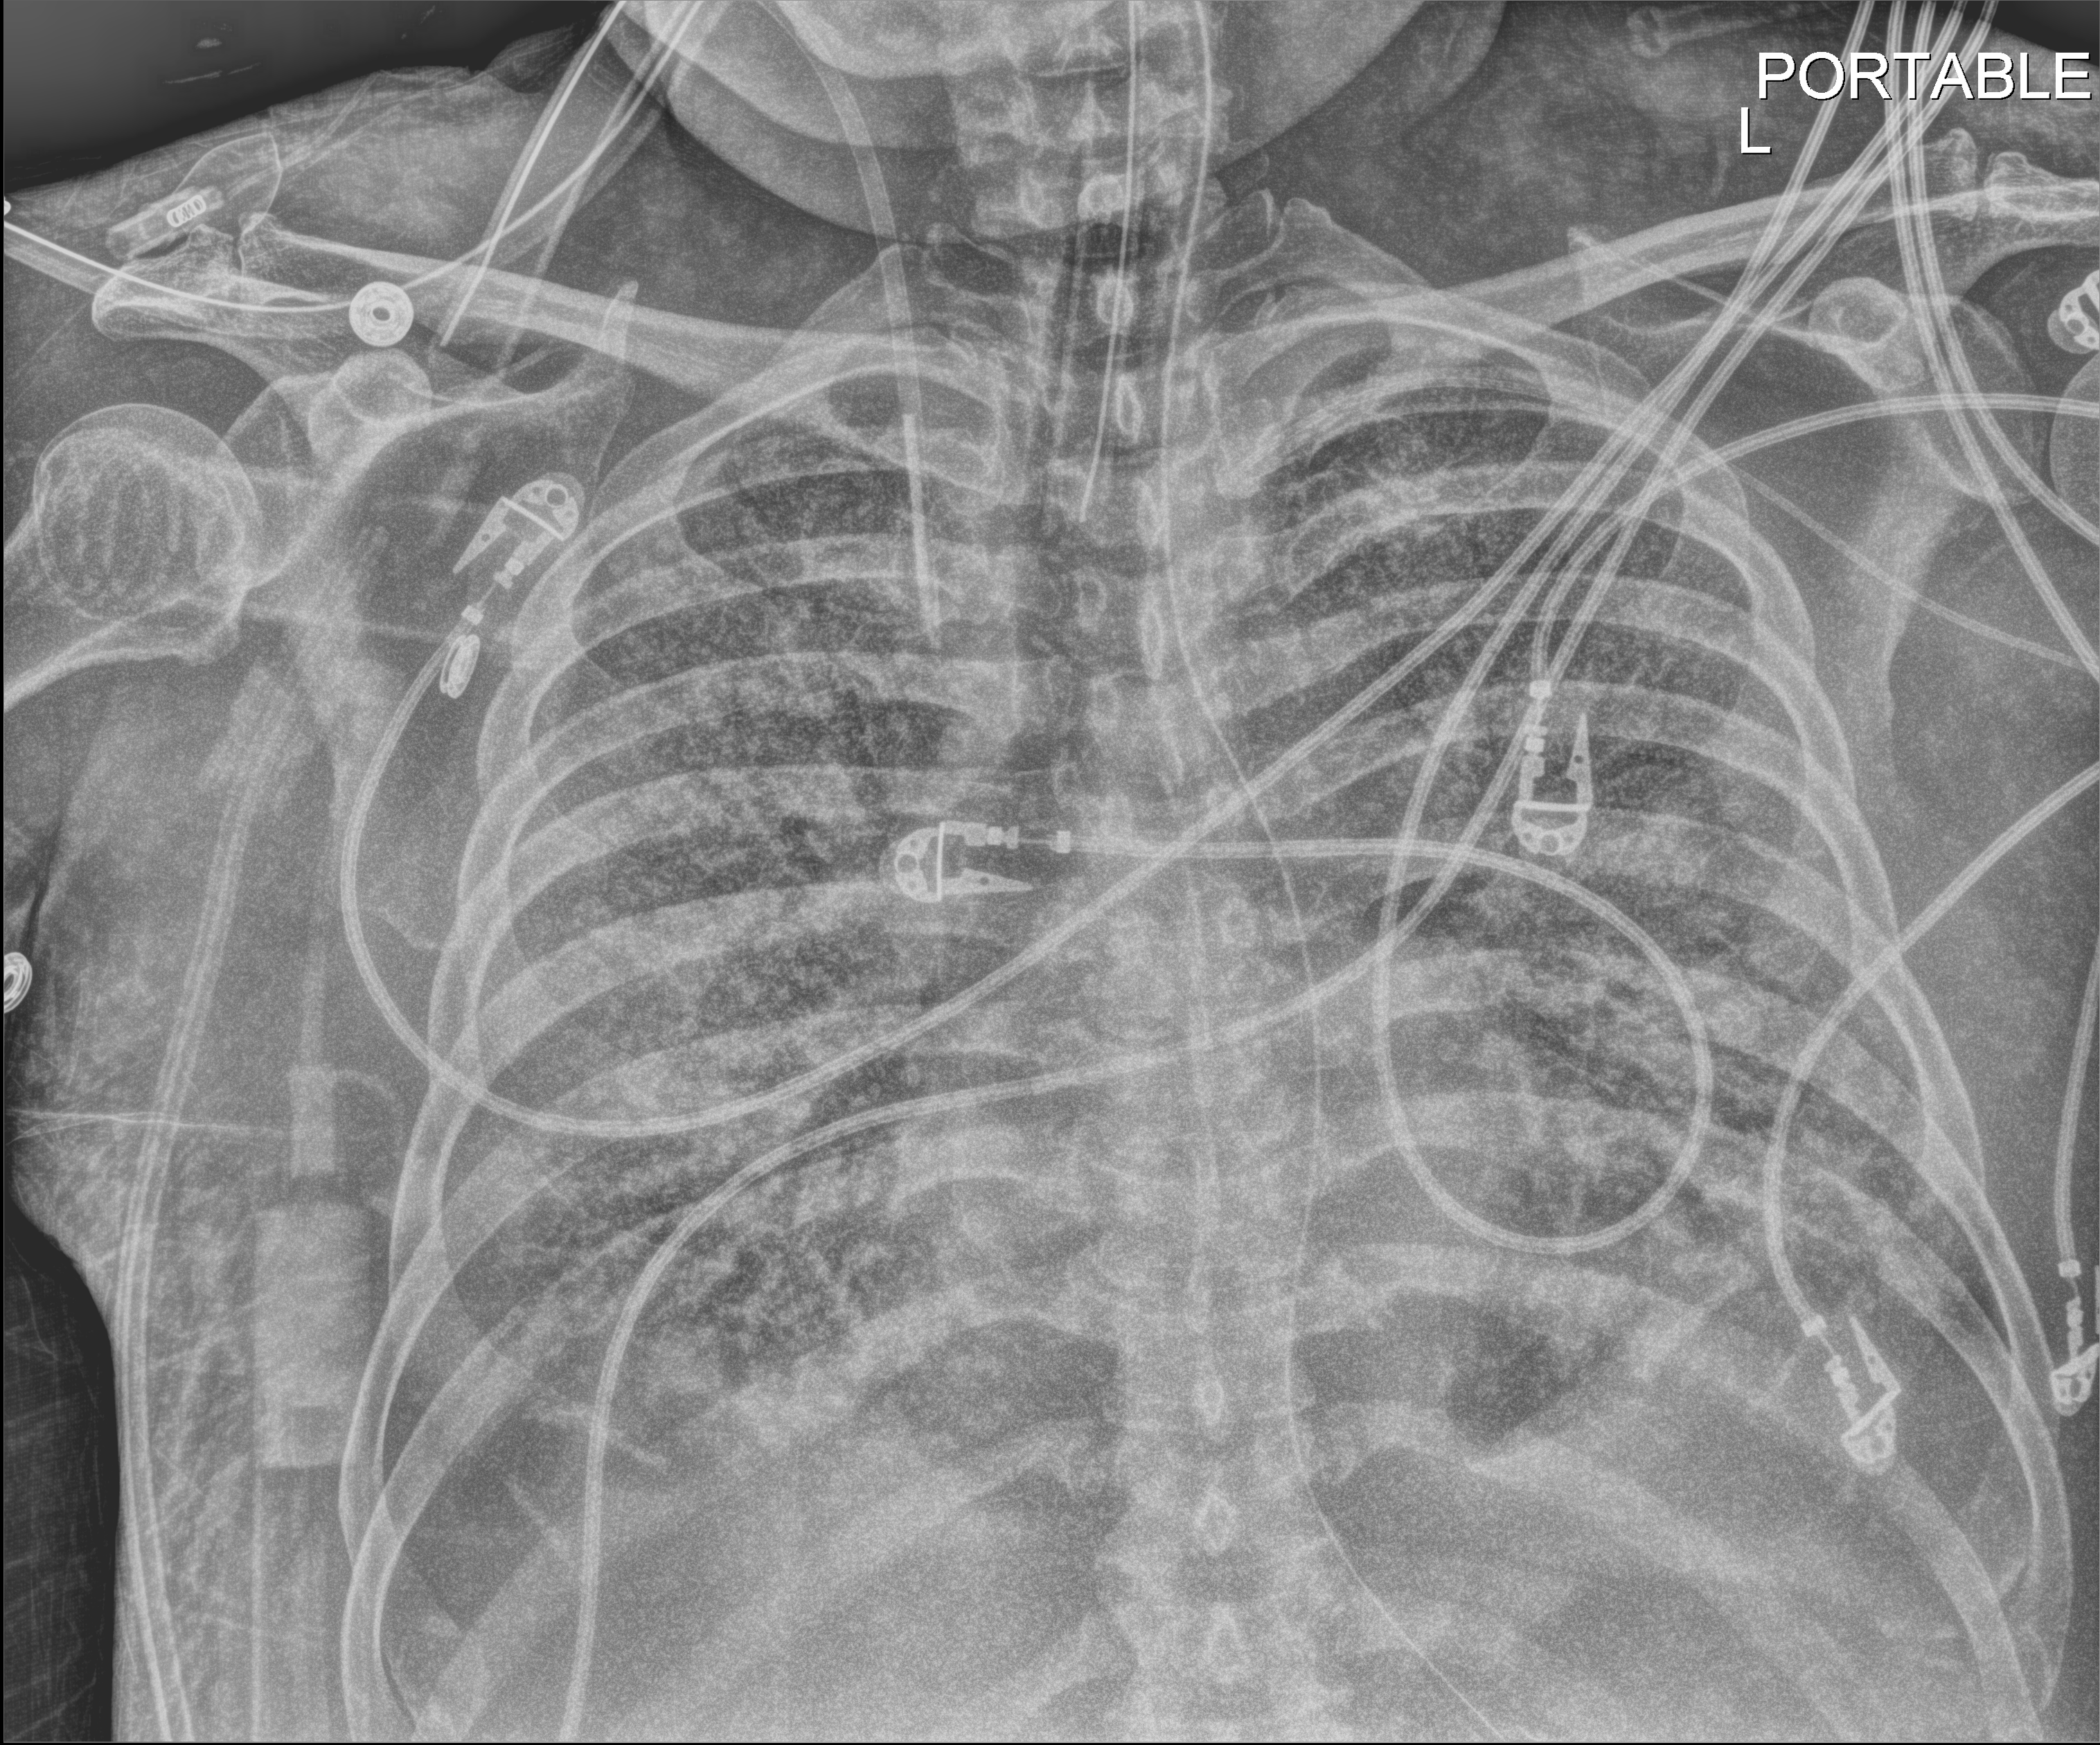
Bedside chest radiograph (digital radiography); anteroposterior (AP) projection. Male patient hospitalised with COVID-19, age 60–74 years.
Admission-level facts for this patient (not findings on this image; timing relative to this image not recorded): smoking status (admission record): never; COPD (admission record): no; mechanically ventilated during this hospital stay: yes.